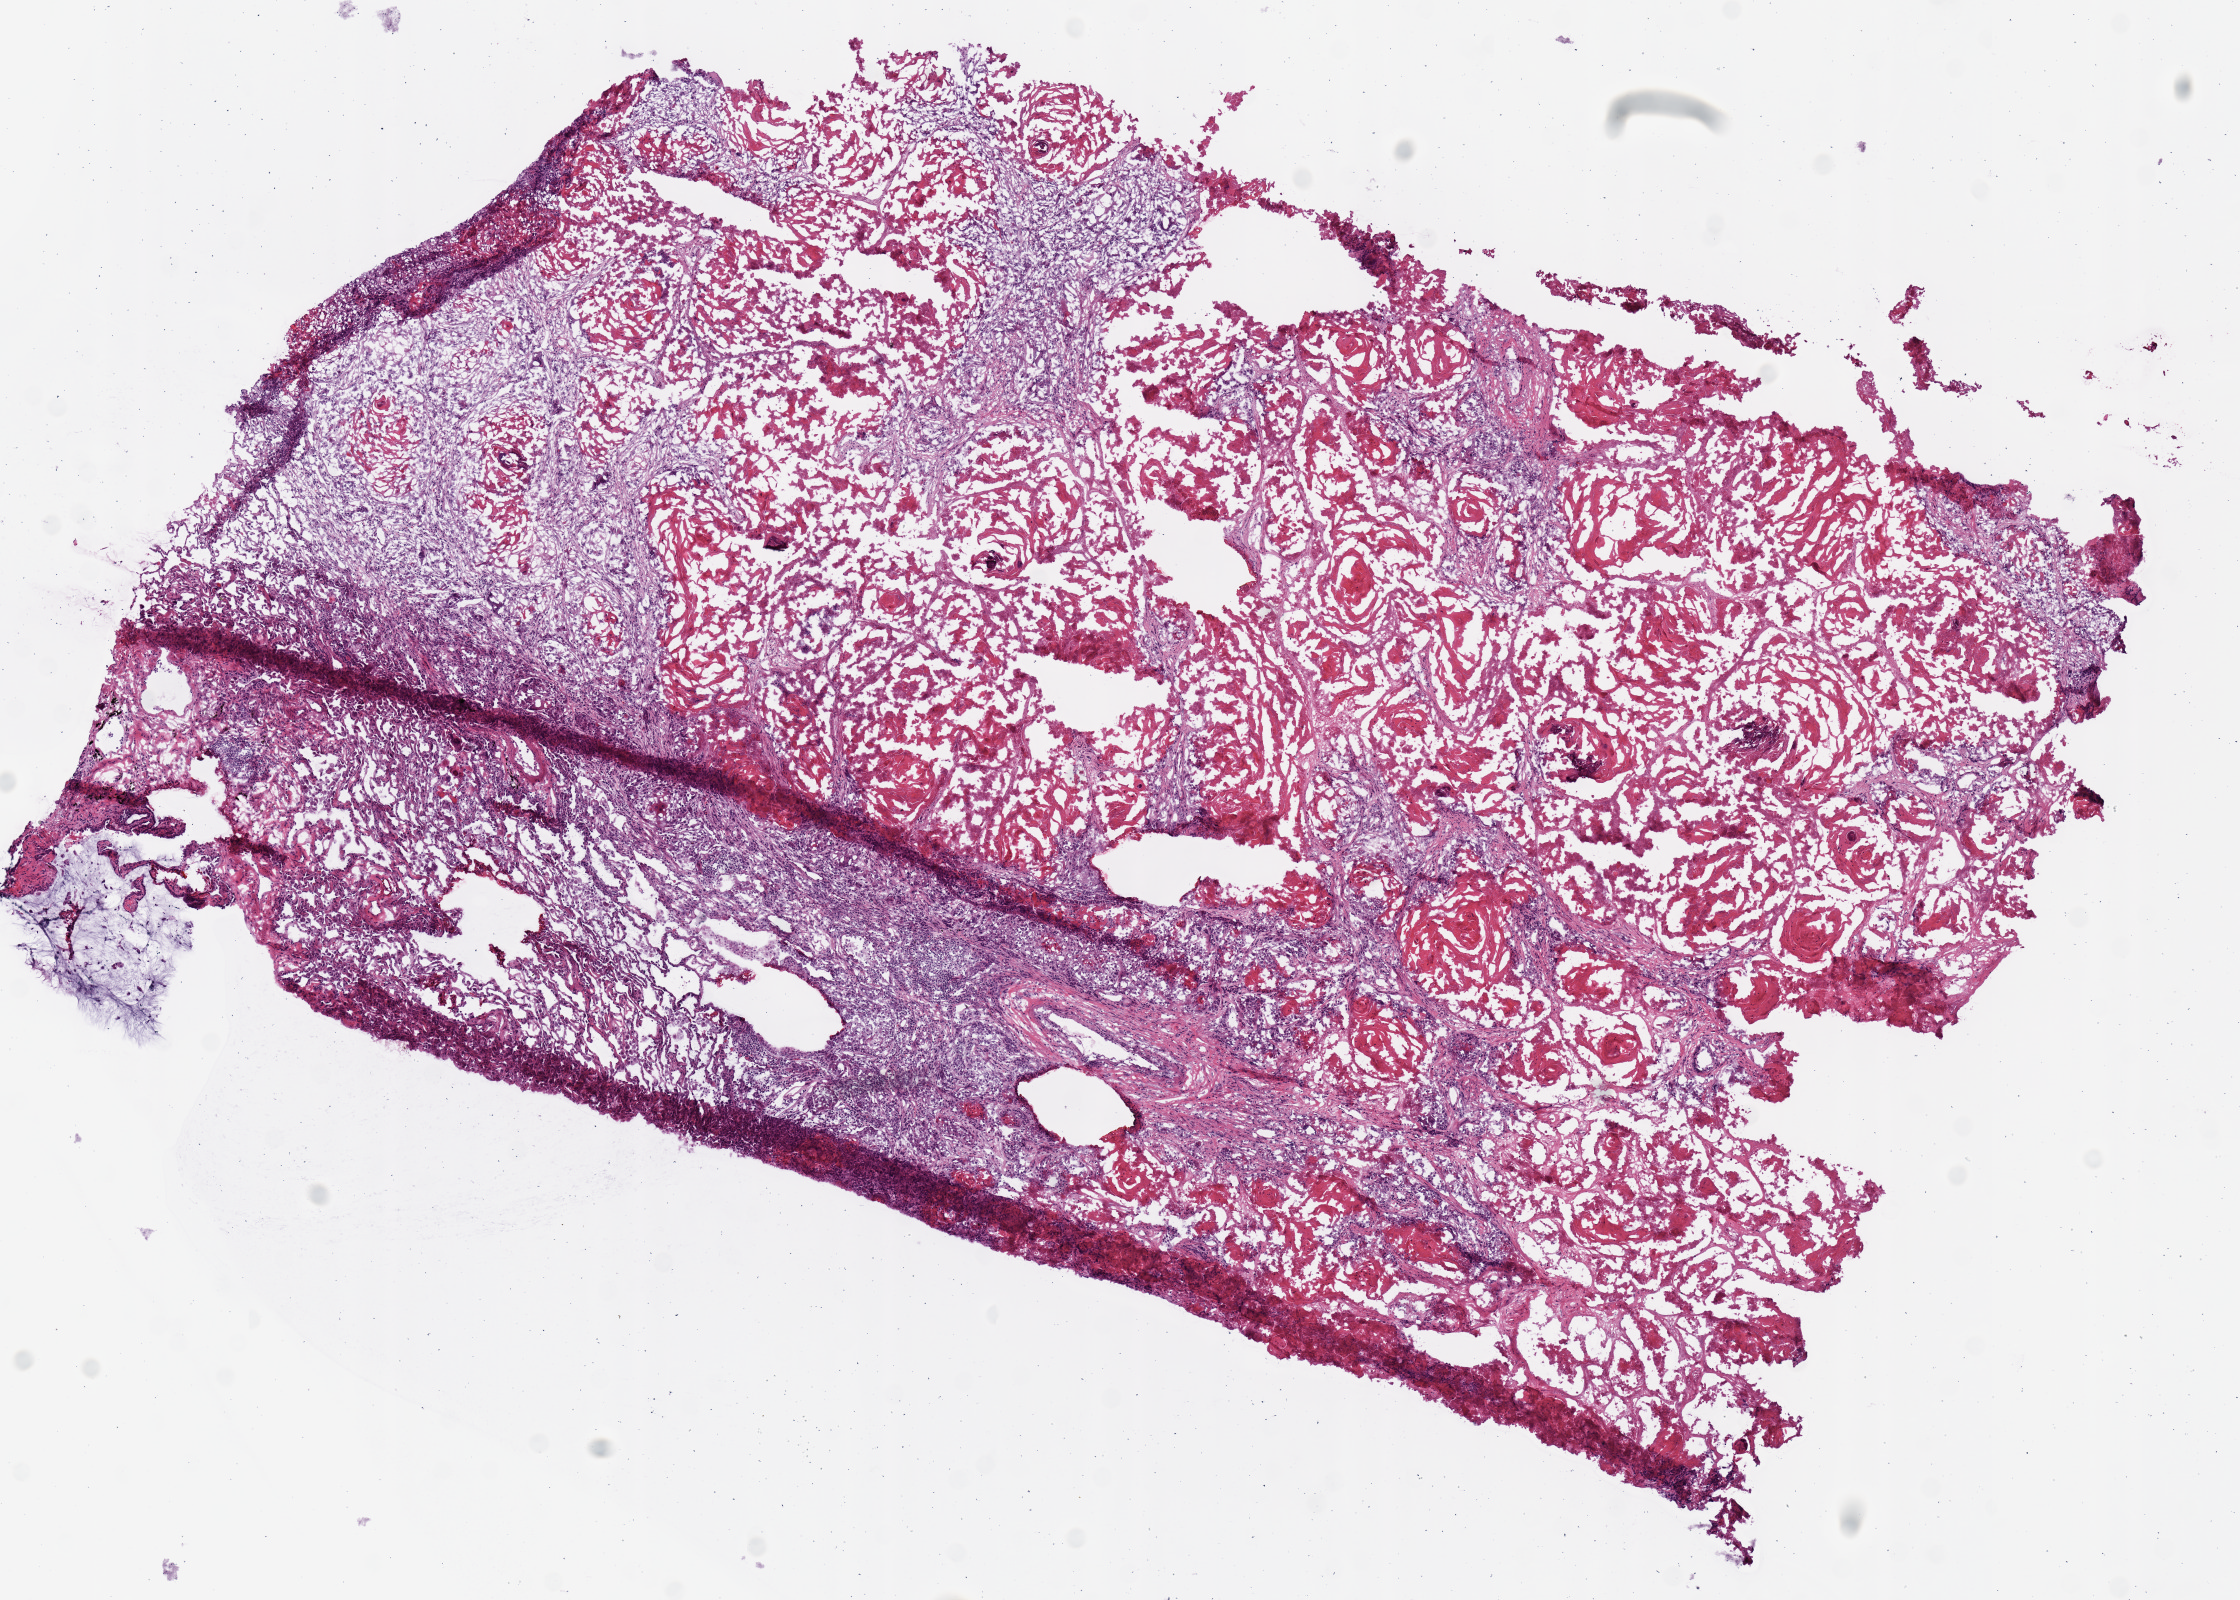
Whole-slide histology image, Hematoxylin and eosin (H&E) stained, low-resolution overview of the scanned area, about 8.9 x 6.3 mm (slide scanned at 20x). Frozen section from the top of the tissue portion. Sample: primary tumour, lung. Male patient; age at initial diagnosis 72 years. Composition of this section per pathologist review: tumour cells 70%, tumour nuclei 60%, normal cells 0%, stromal cells 10%, necrosis 20%.
Pathologic diagnosis: Squamous cell carcinoma, NOS (lower lobe, lung). AJCC pathologic stage: IB (6th edition).